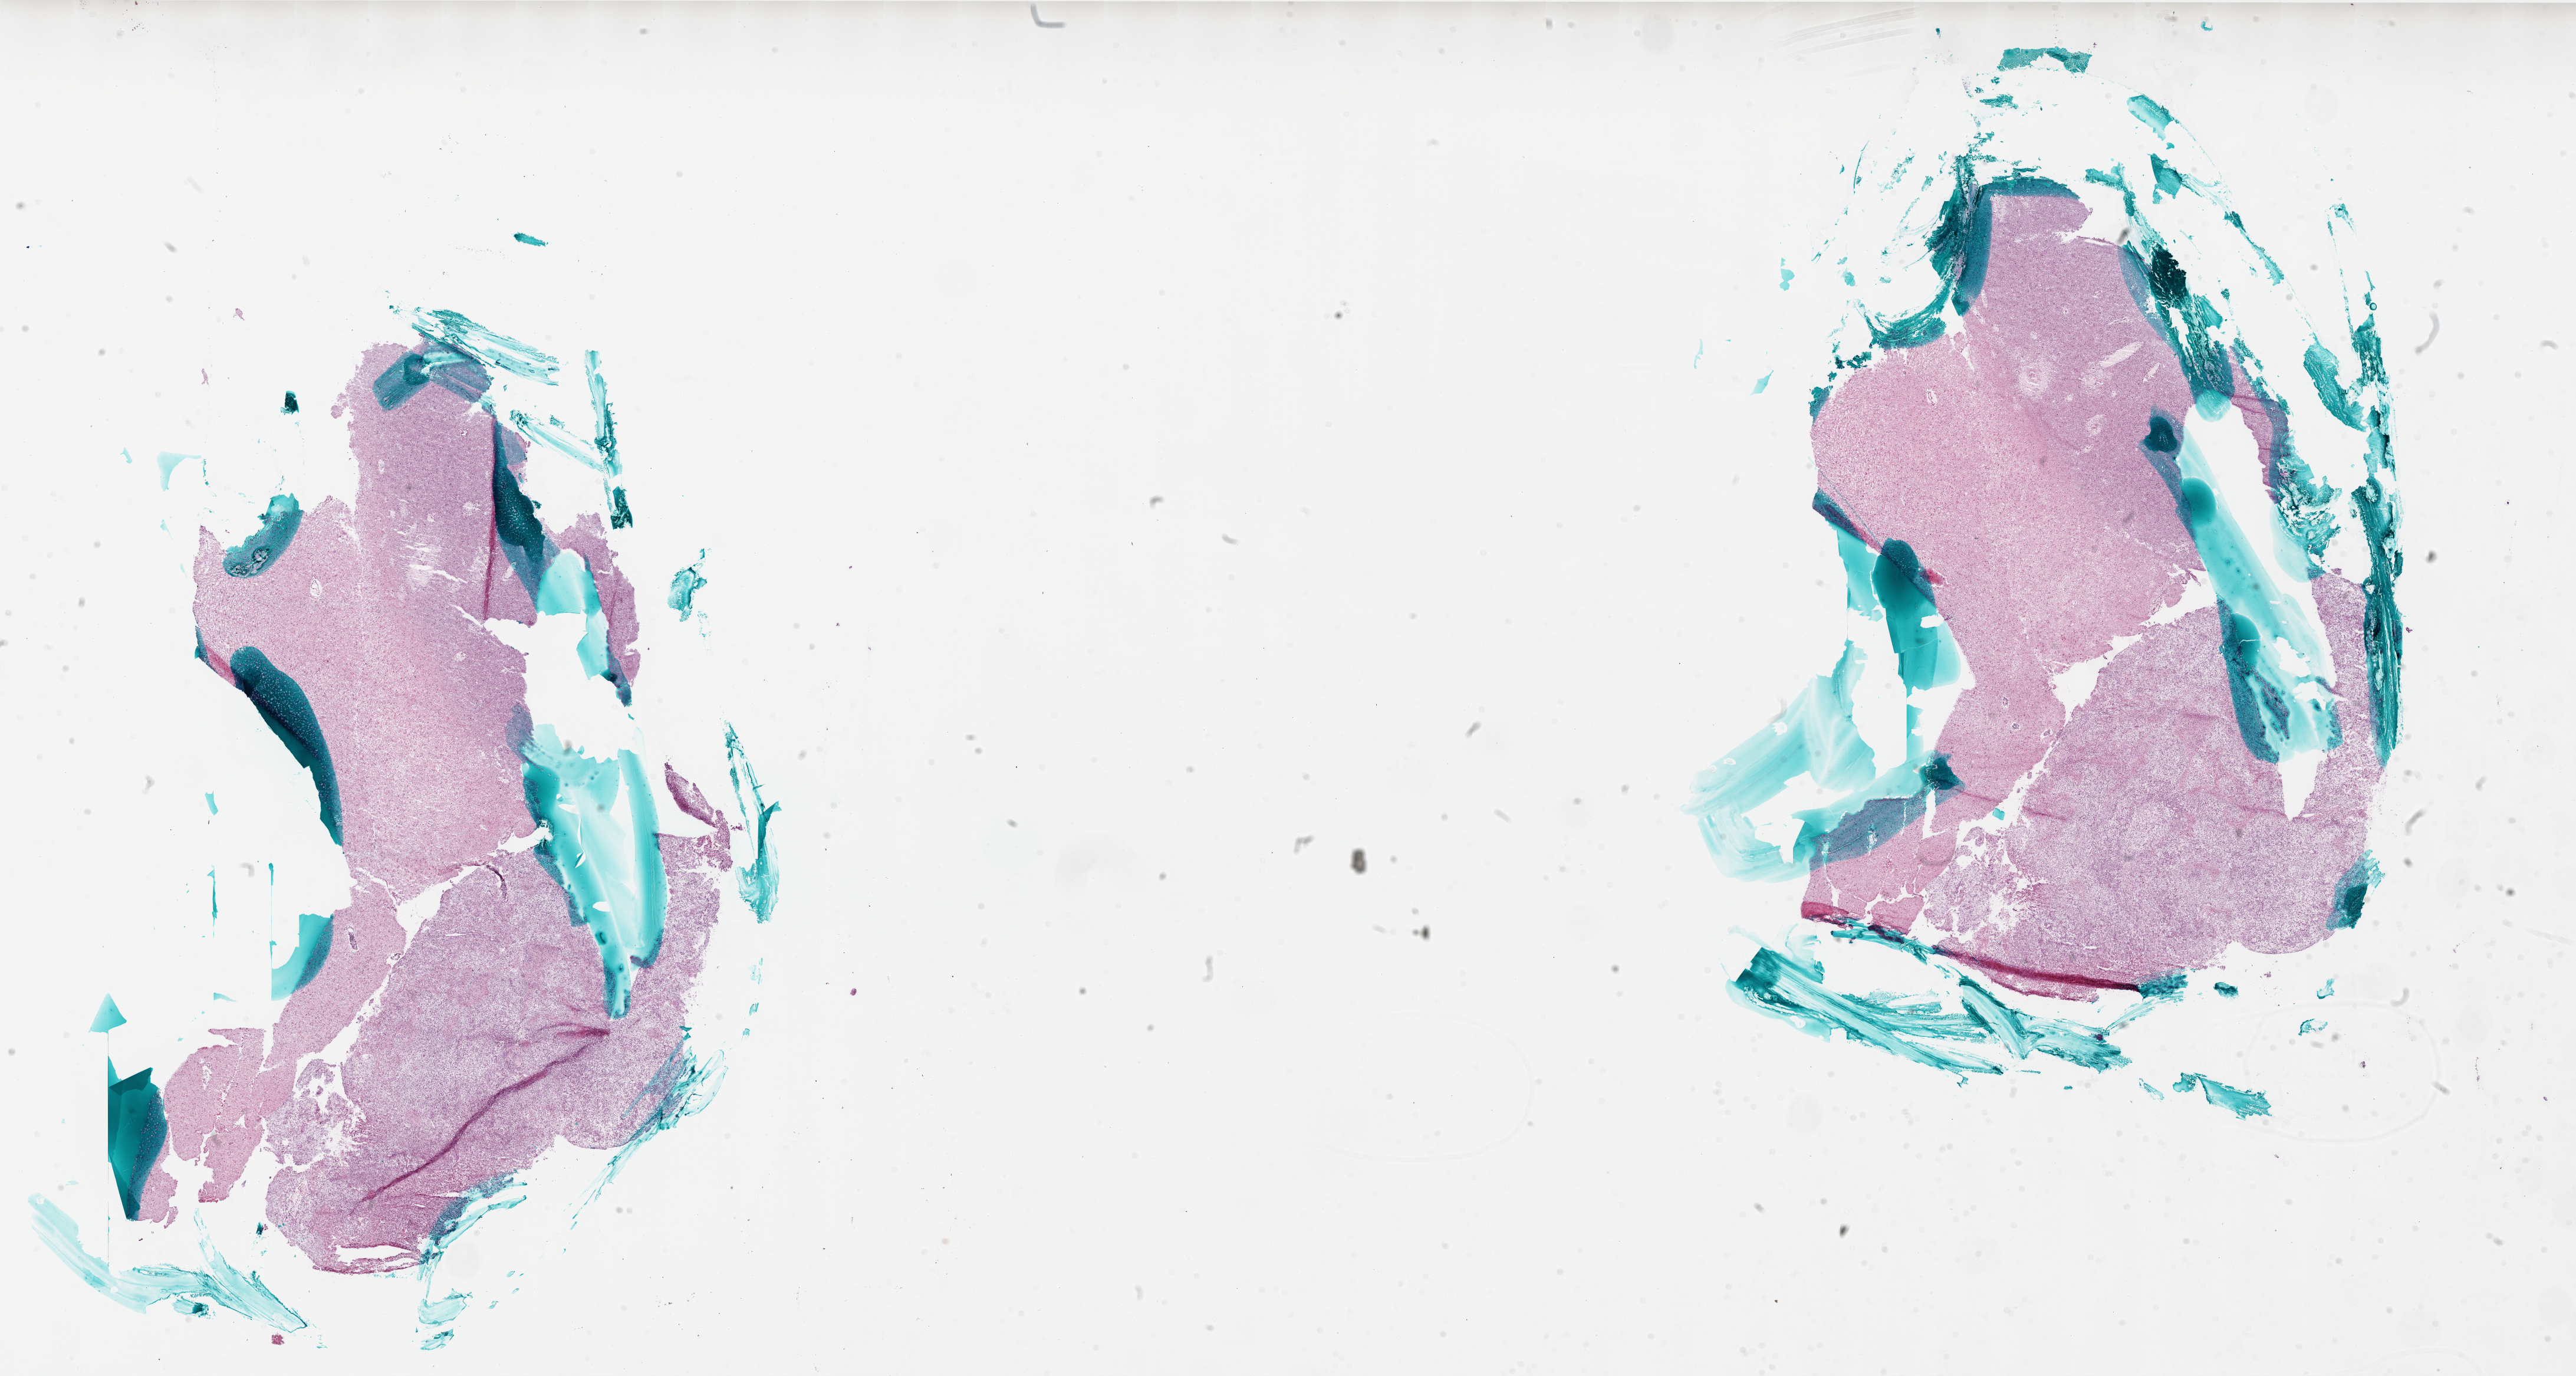
Digitized H&E tissue section (whole slide), shown as a low-resolution overview of the whole scanned area (about 35.0 x 18.7 mm). Frozen section. Sample: primary tumour, brain. Female patient; age at initial diagnosis 63 years. Composition of this section per pathologist review: tumour cells 75%, tumour nuclei 95%, normal cells 0%, stromal cells 25%, necrosis 0%.
- histologic diagnosis: Glioblastoma